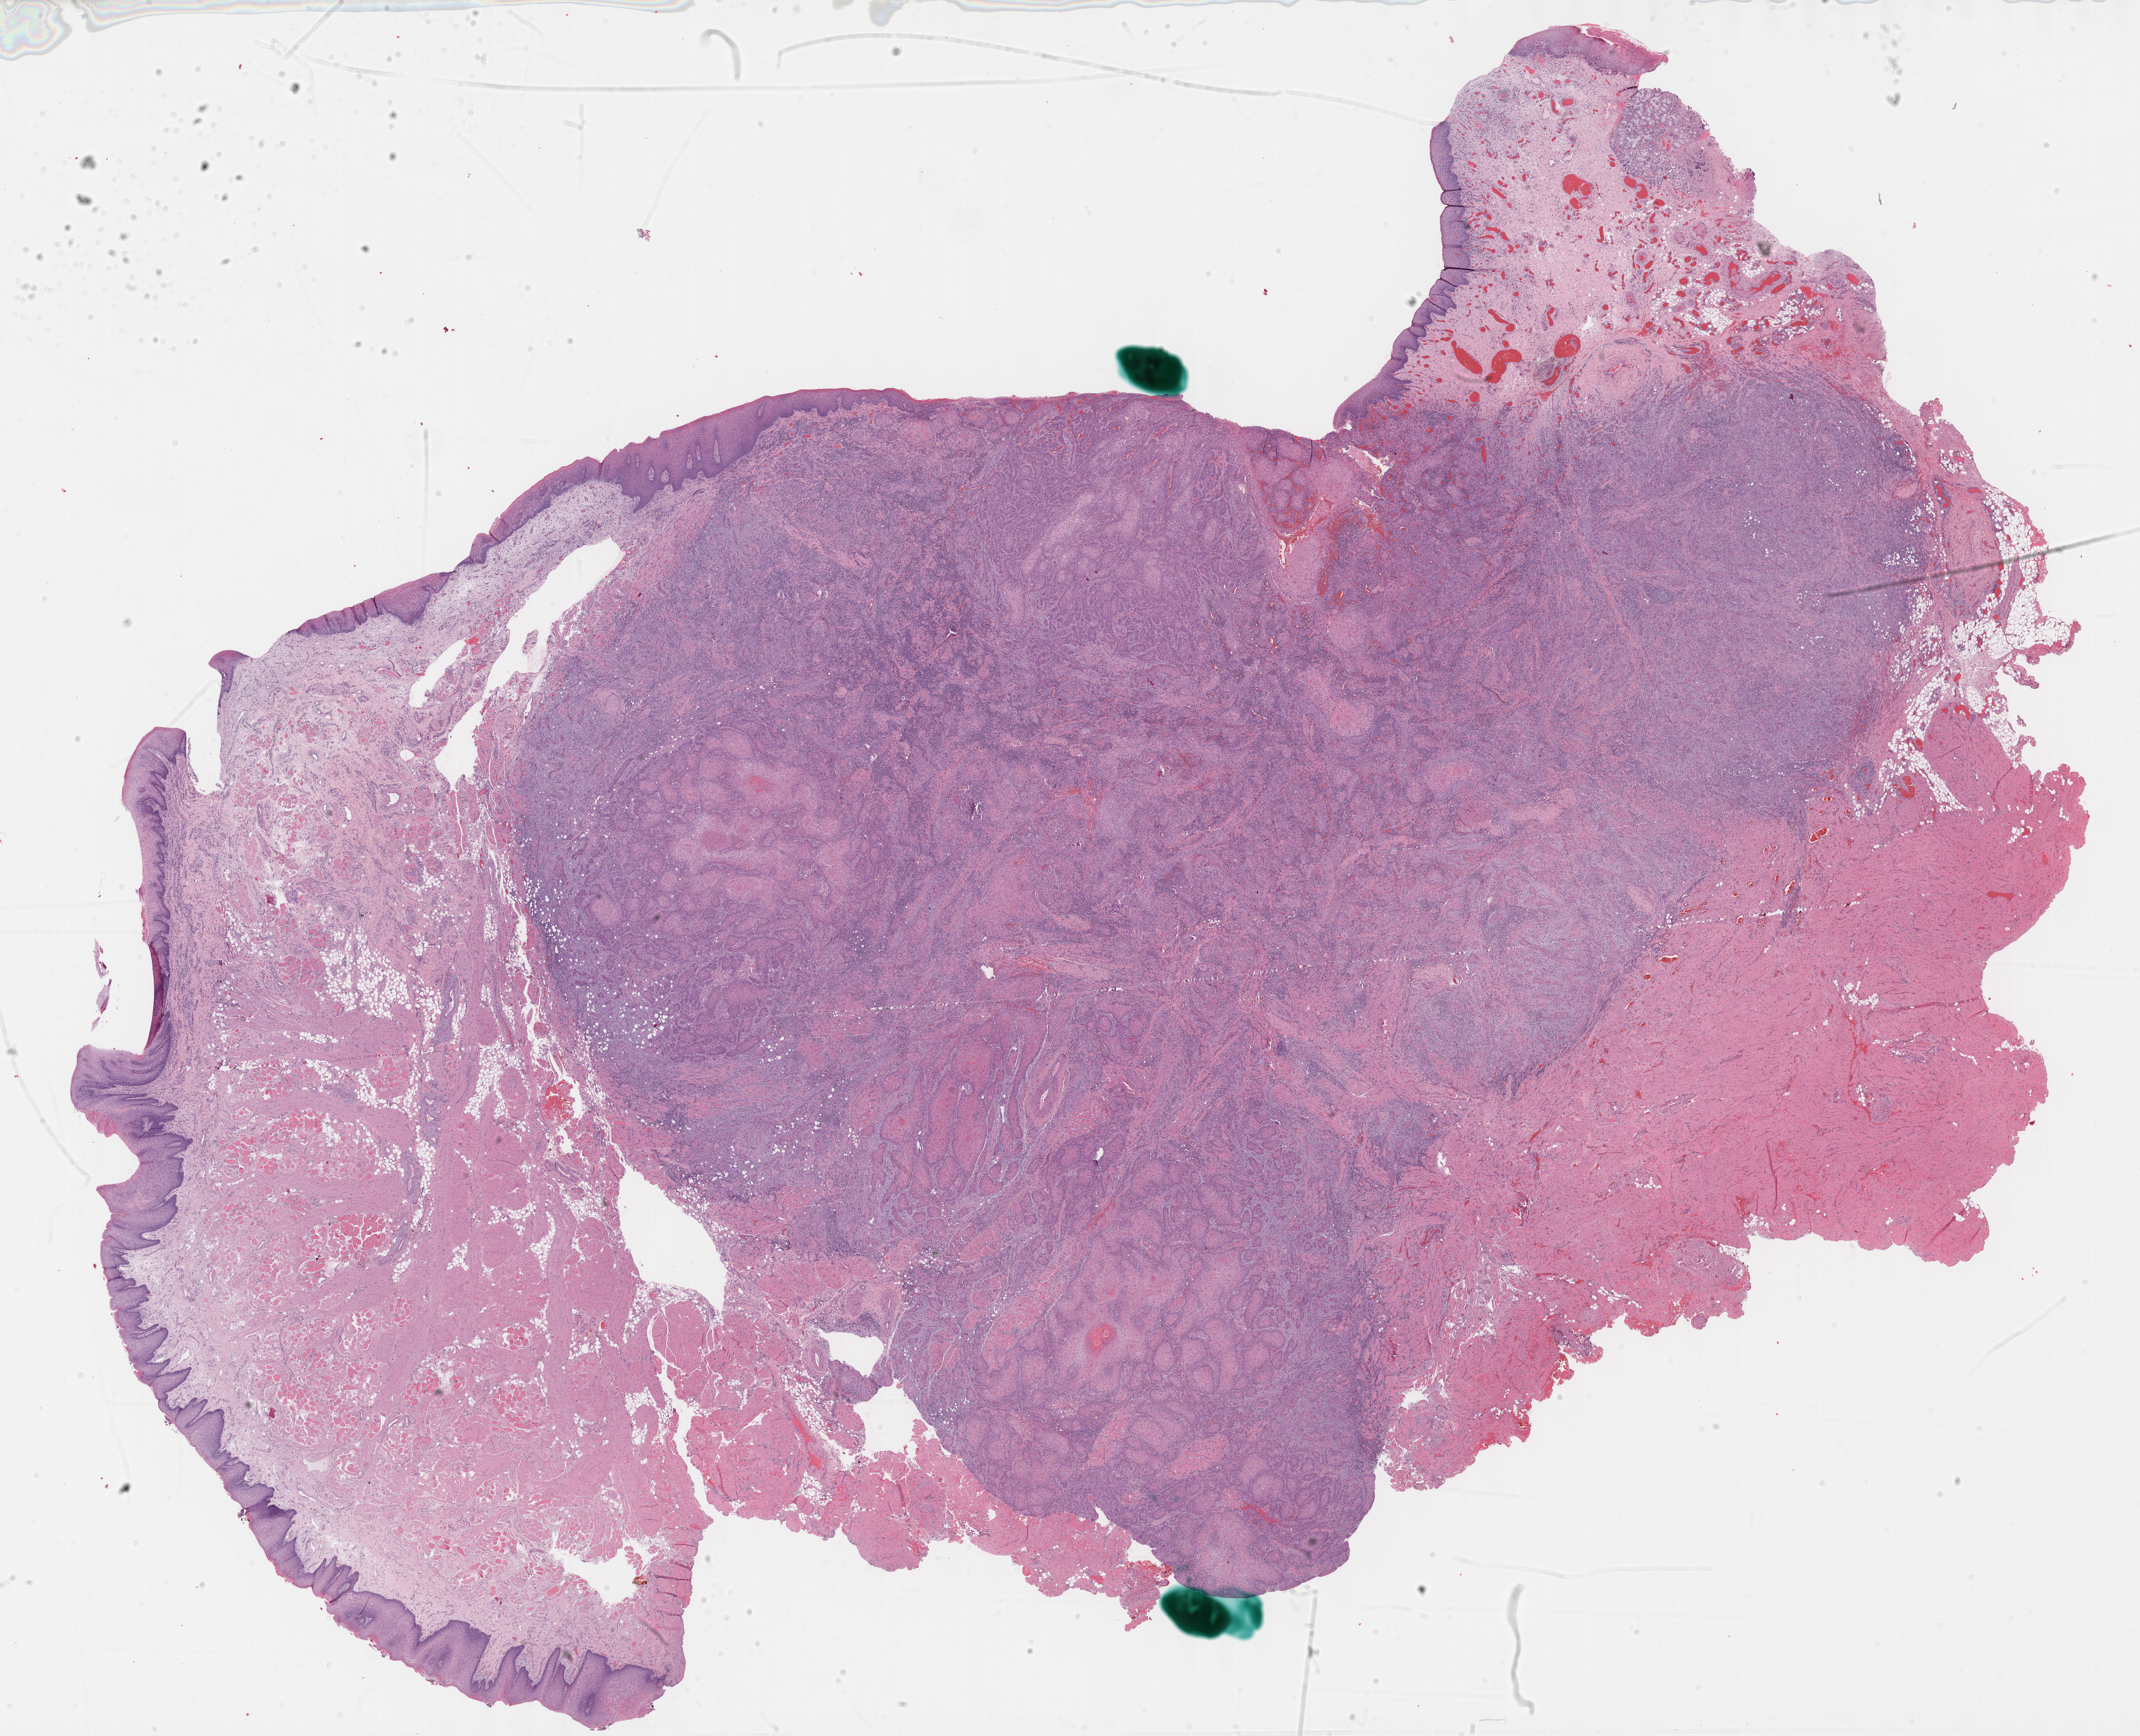
Whole-slide histology image, H&E-stained, a low-resolution overview of the entire scanned area, about 27.7 x 22.4 mm, formalin-fixed paraffin-embedded (FFPE) diagnostic section, sample: primary tumour, head and neck. Male, age 65 years at initial diagnosis.
Diagnosis: Squamous cell carcinoma, NOS.